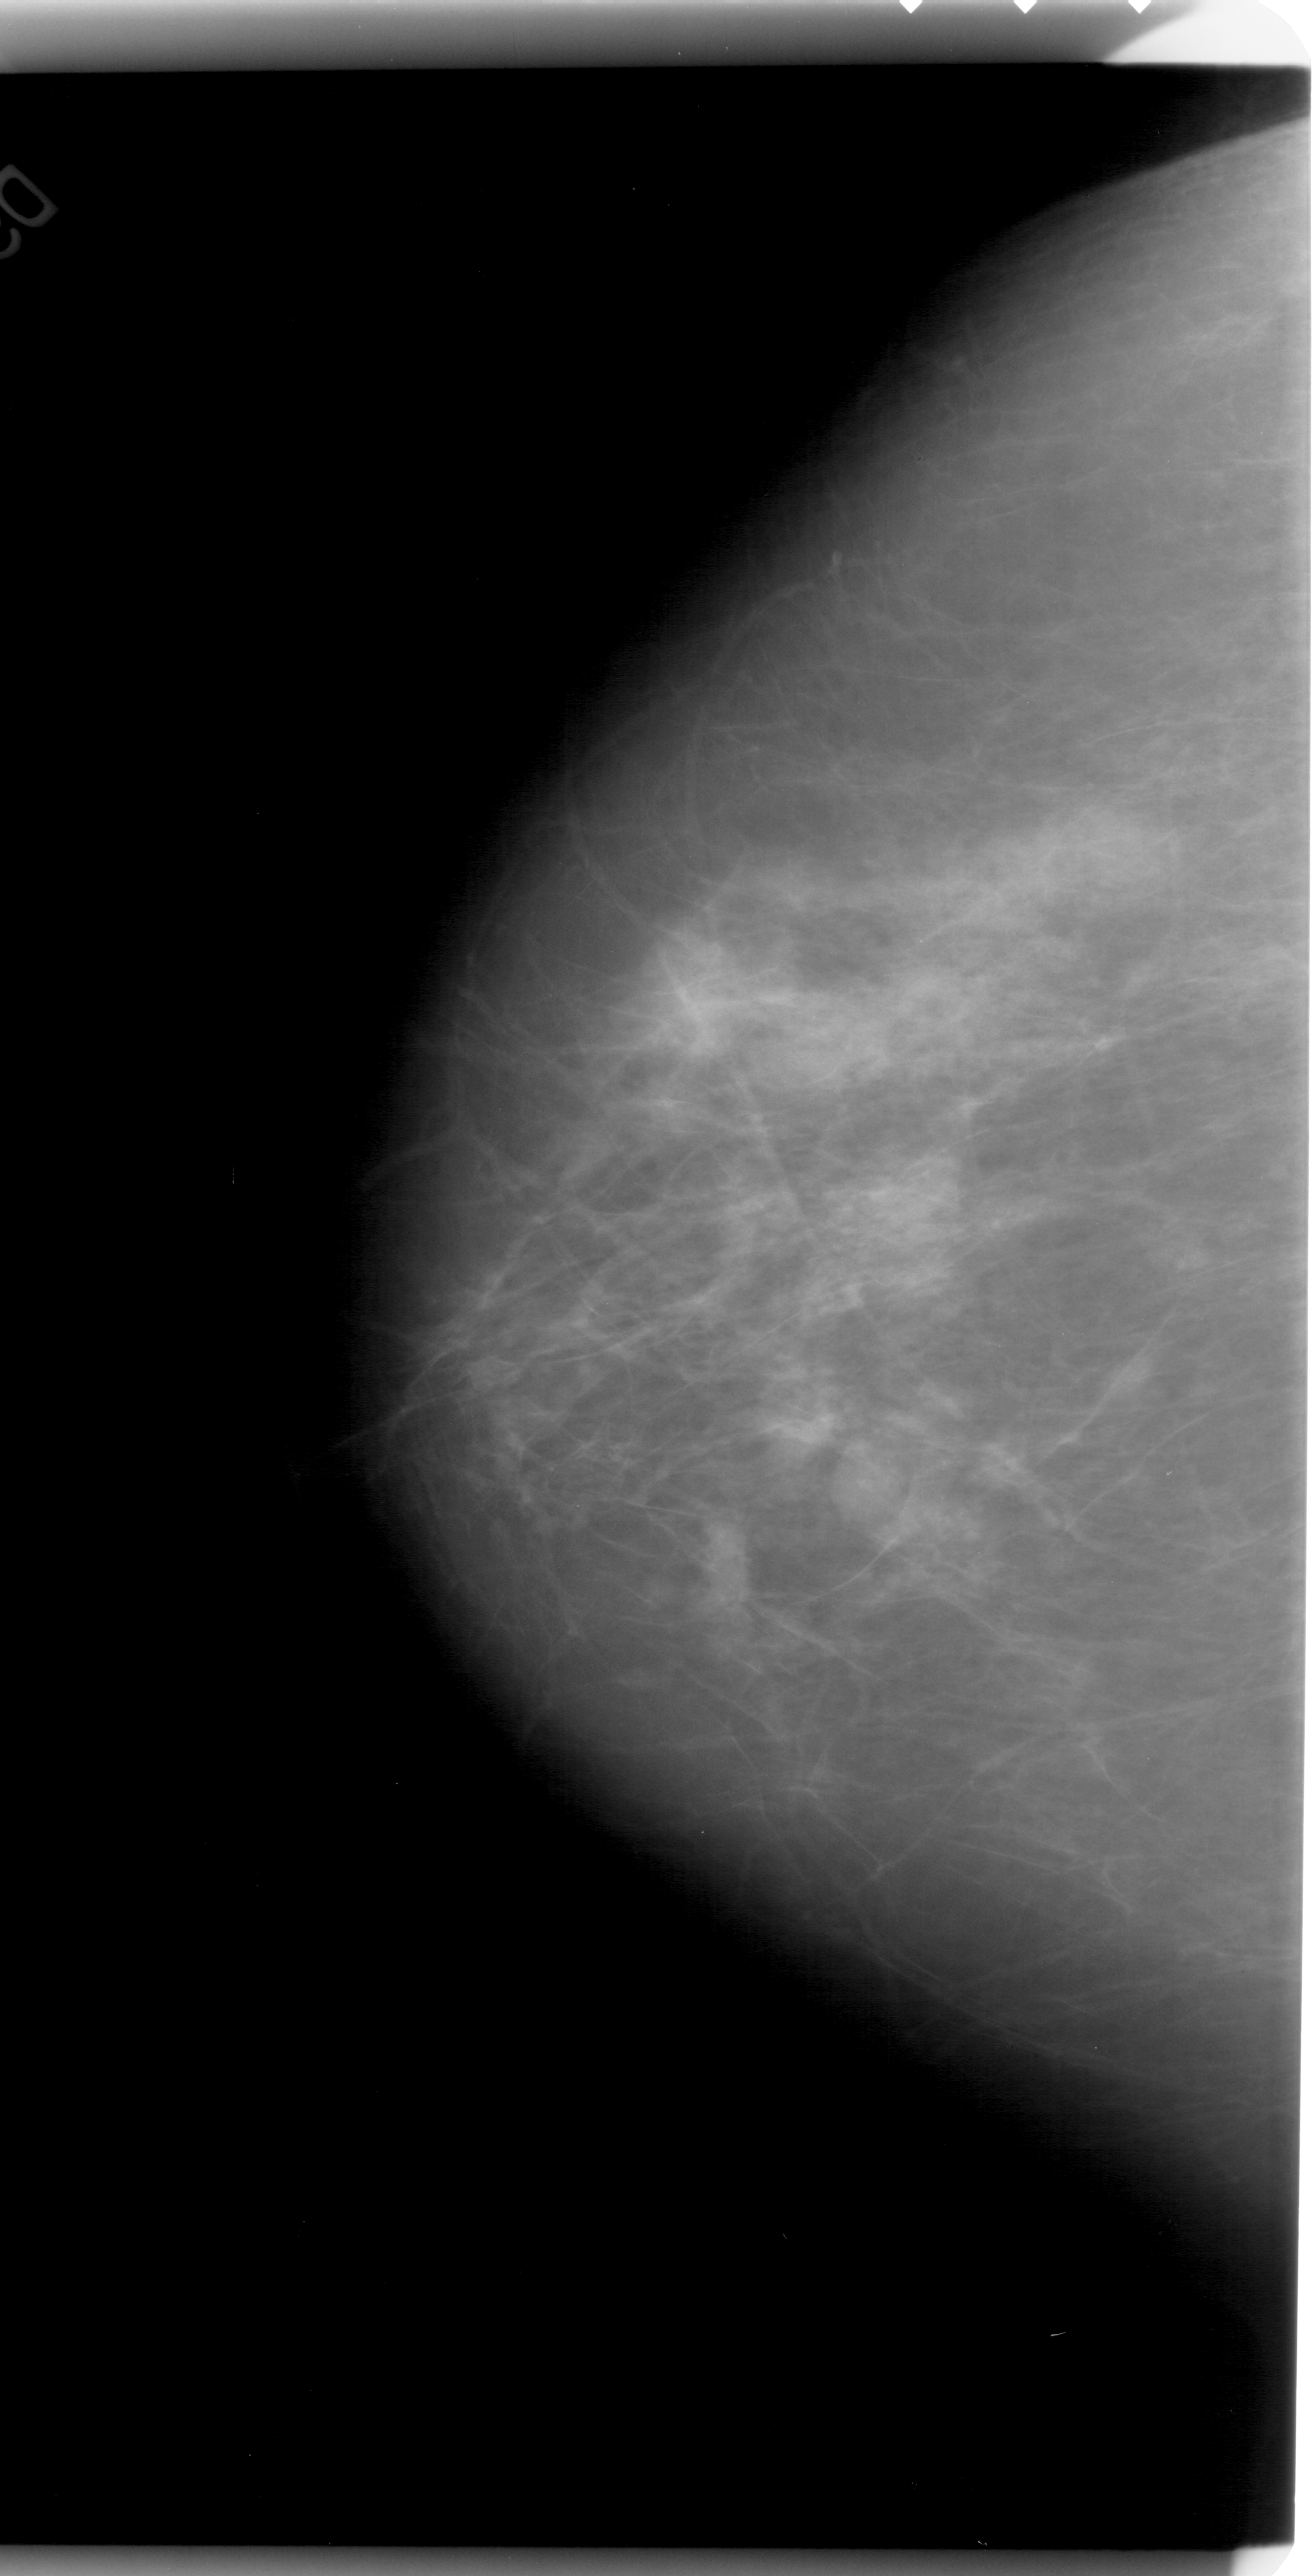
Scanned film-screen mammogram. Left breast. CC view. Breast composition: scattered fibroglandular densities (BI-RADS density category 2 of 4). 1314 × 2576 image matrix.
Expert-marked regions of interest on this film, with their recorded descriptors:
- mass, shape oval, margins obscured; BI-RADS assessment category 3; pathology (as recorded): benign: box from (x=823, y=1435) to (x=904, y=1525) px